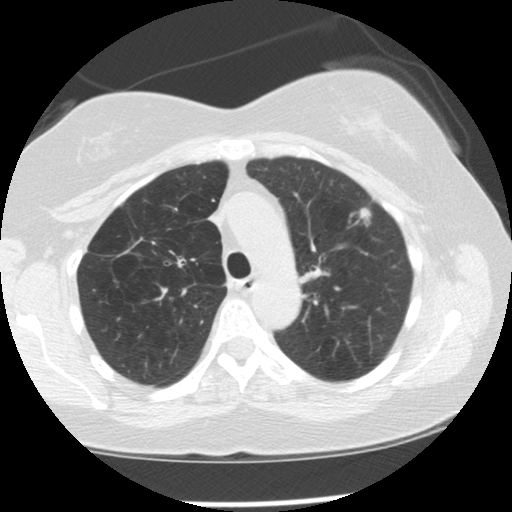
Low-dose screening chest CT, one axial slice; slice 91 of 128 in the series (ordered by position); reconstruction kernel STANDARD; 120 kVp; lung window (W 1500 / L -600 HU); 512 × 512 image matrix, field of view 319 × 319 mm.
Outlined on this slice (manually delineated by an expert):
- lesion 1 (tumor, upper lobe of left lung): bounding box [x1, y1, x2, y2] px = [359, 208, 372, 227]